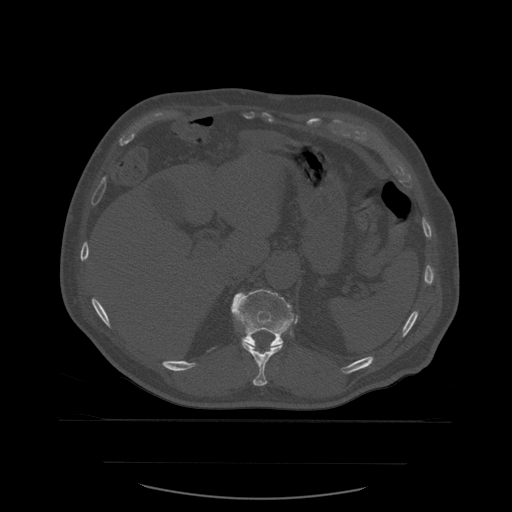
CT including the spine, one axial slice; slice 285 of 590 in the series (ordered by position); bone window (W 1800 / L 400 HU); 1.25 mm slice thickness; 512 × 512 image matrix, field of view 479 × 479 mm. Patient age 71 years. Case-level facts recorded for this patient, not image findings: primary cancer: lung.
Structures marked on this image (semi-automatically segmented with operator editing):
- T11 vertebra: box from (x=241, y=343) to (x=283, y=386) px
- T12 vertebra: (x=231, y=289)–(x=298, y=348)